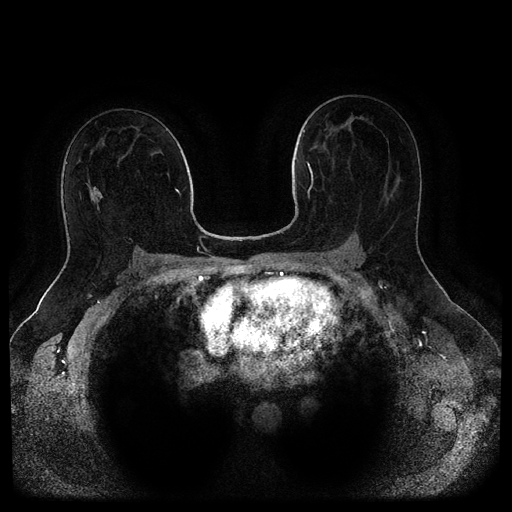
Breast MRI (dynamic contrast-enhanced, multi-phase), one axial slice; slice 56 of 116 in the series (ordered by position); dynamic contrast-enhanced series, time point 2 of 5 at this slice position (early post-contrast); 1.5 T; TE 2.6 ms, TR 5.3 ms; 2 mm slice thickness; 512 × 512 image matrix. Patient: female, 44 years.
Outlined on this slice (semi-automatically segmented with operator editing):
- breast lesion (labelled benign in the annotation): bounding box [x1, y1, x2, y2] px = [91, 187, 103, 207]